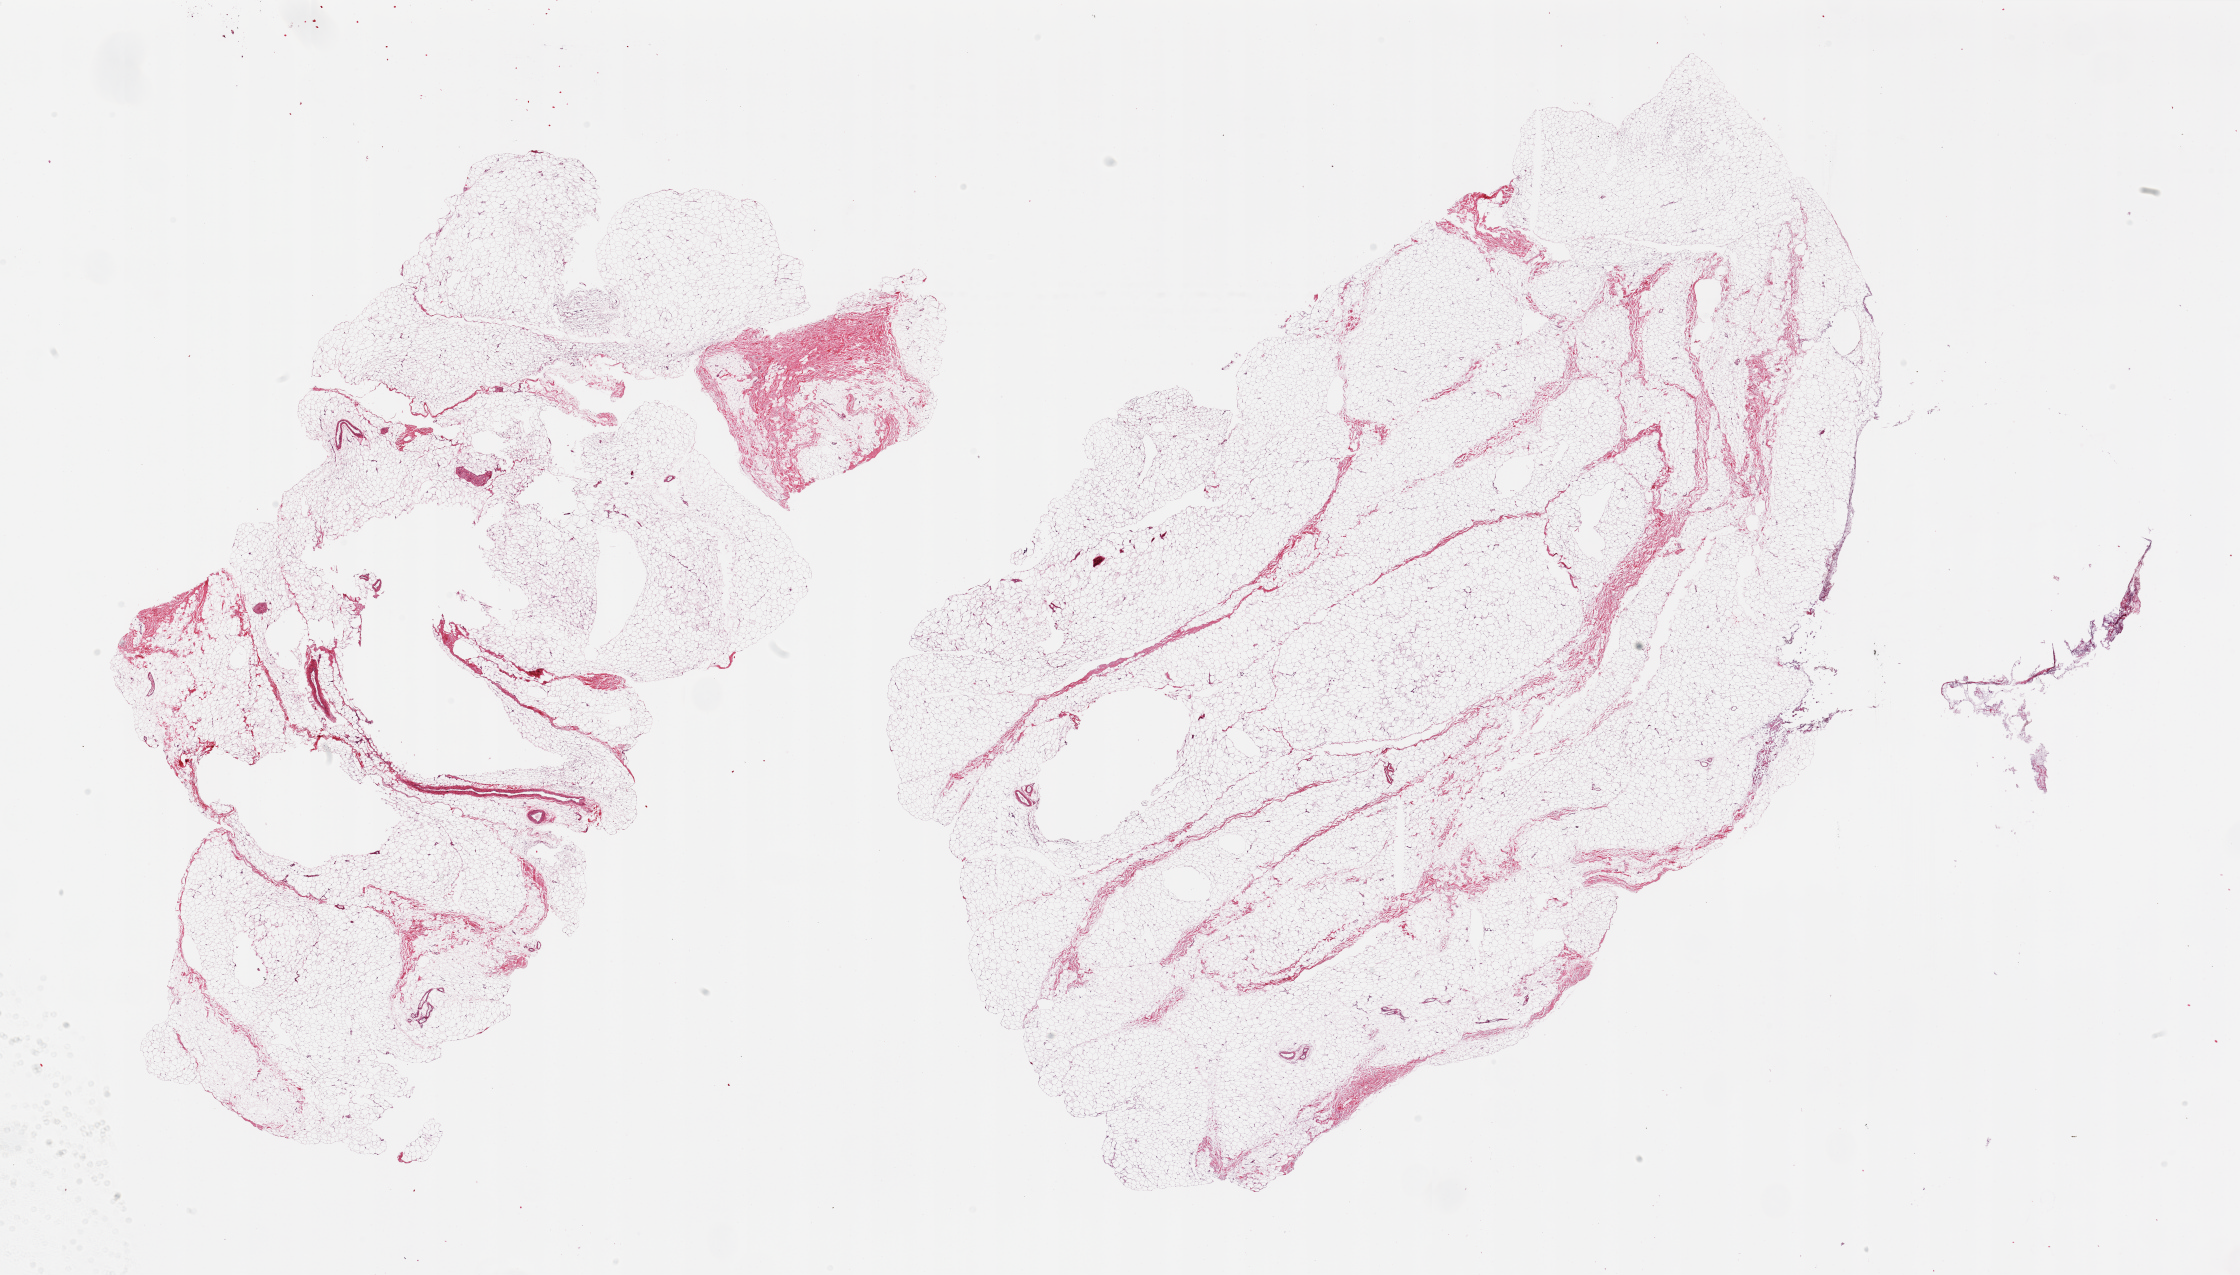
Whole-slide image, hematoxylin and eosin (H&E) stain, whole scanned area (about 35.4 x 20.2 mm, acquisition: 20x scan) shown as a low-resolution overview, PAXgene-fixed paraffin-embedded (PFPE) section, target tissue: breast, donor tissue sample.
Reviewer comment on this tissue sample: 2 pieces, fibroadipose elements only; no ductal elements noted.